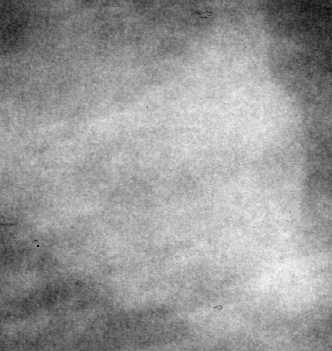
Region of interest cut from a scanned film mammogram (one marked finding); left breast; CC view.
Marked abnormality: mass, shape lobulated, margins circumscribed; BI-RADS assessment category 4; pathology (as recorded): benign.